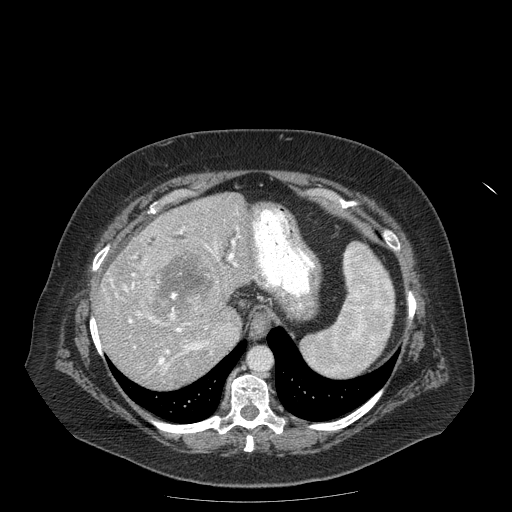
Contrast-enhanced abdominal CT (liver protocol), one axial slice; slice 141 of 204 in the series (ordered by position); reconstruction kernel STANDARD; soft-tissue window (W 400 / L 40 HU); 2.5 mm slice thickness; 512 × 512 image matrix, field of view 440 × 440 mm. Case-level facts recorded for this patient, not image findings: diagnosis: hepatocellular carcinoma (patient treated with transarterial chemoembolisation; whether this scan precedes or follows treatment is not stated here); TNM stage (as recorded): Stage-IIIB; Child-Pugh class: A; tumour differentiation: well differentiated.
Outlined on this slice (semi-automatic segmentation, software-assisted and operator-edited):
- liver parenchyma outside the tumour (the mass and vessels are separate outlines, so this box may not span the whole liver): bounding box (x1, y1, x2, y2) in pixels: (95, 192, 254, 388)
- mass: (140, 238, 224, 325)
- liver vessels: (107, 226, 239, 371)